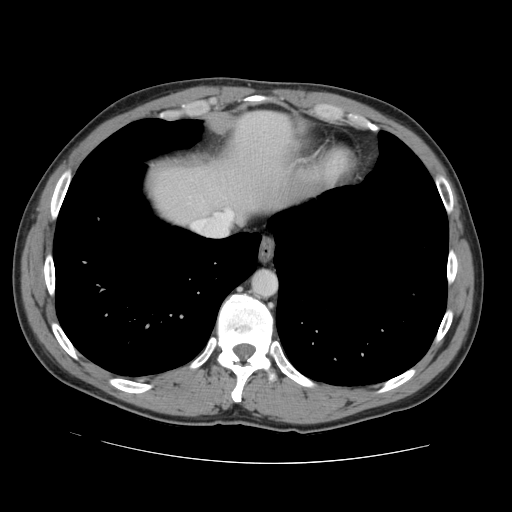
Contrast-enhanced abdominal CT, one axial slice. Slice 127 of 131 in the series (ordered by position). 120 kVp. Intravenous contrast given. Soft-tissue window (W 400 / L 40 HU). 2.5 mm slice thickness. 512 × 512 image matrix, field of view 380 × 380 mm. Male patient, age 40 years. Case-level facts recorded for this patient, not image findings: diagnosis: colorectal cancer liver metastases, imaged before liver resection; multiple liver metastases: yes; largest metastasis: 2.9 cm; chemotherapy before resection: yes.
Annotated regions visible in this slice (outlined manually by an expert reader):
- hepatic veins: bounding box [x1, y1, x2, y2] px = [192, 210, 234, 236]
- liver: [150, 113, 291, 222]
- planned liver remnant (the part of the liver to remain after resection): [150, 113, 298, 221]